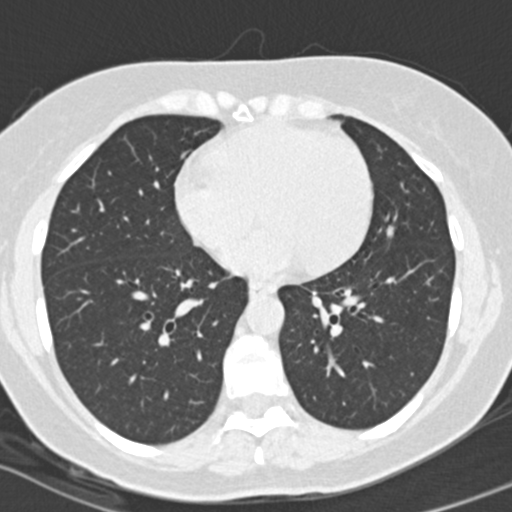
Chest CT (low-dose screening protocol), one axial image, baseline annual screen, lung window (W 1500 / L -600 HU), 2 mm slice thickness, standard (soft-tissue) reconstruction kernel (B30f), 120 kVp, slice 91 of 151 in the series. Female, age 56 years at enrolment.
Expert reader's lesion annotation, bounding box [x1, y1, x2, y2] px = [368, 212, 409, 255]. Screening reader's record for this exam (one nodule recorded; not confirmed to be the boxed lesion): non-calcified nodule or mass ≥4 mm, lingula, 7 × 5 mm, smooth margins, soft tissue attenuation. Official screen result: positive, change unspecified: nodule(s) >= 4 mm or enlarging nodule(s), mass(es), or other non-specific abnormalities suspicious for lung cancer.